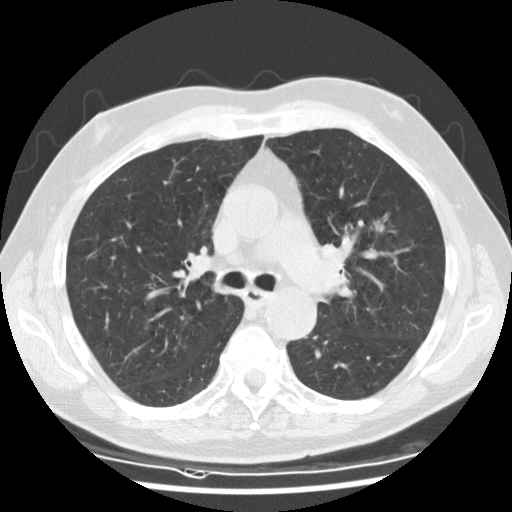
Axial slice from a low-dose chest CT screening exam; baseline screening round; lung window (W 1500 / L -600 HU); 120 kVp; 512 × 512 image matrix, field of view 340 × 340 mm. Male, age 73 years at enrolment.
Expert-annotated lung lesion, box from (x=353, y=201) to (x=409, y=256) px. Reader record for this screening exam (exam-level; its link to the box is not recorded): non-calcified nodule or mass ≥4 mm, right lower lobe, 13 × 13 mm, smooth margins, soft tissue attenuation. Note: the box lies in the patient's left hemithorax on this image, whereas the reader's record names the right lung; they may be different findings. Official screen result: positive, change unspecified: nodule(s) >= 4 mm or enlarging nodule(s), mass(es), or other non-specific abnormalities suspicious for lung cancer.